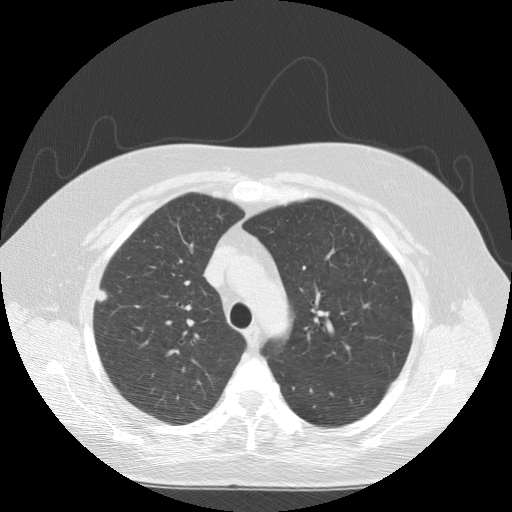
Low-dose screening chest CT, one axial slice; position 110 of 146 along the scan axis; reconstruction kernel STANDARD; 120 kVp; lung window (W 1500 / L -600 HU); 2.5 mm slice thickness; 512 × 512 image matrix.
Annotated regions visible in this slice (manually delineated by an expert):
- lesion 1 (tumor, upper lobe of right lung): bounding box [x1, y1, x2, y2] px = [97, 290, 107, 302]